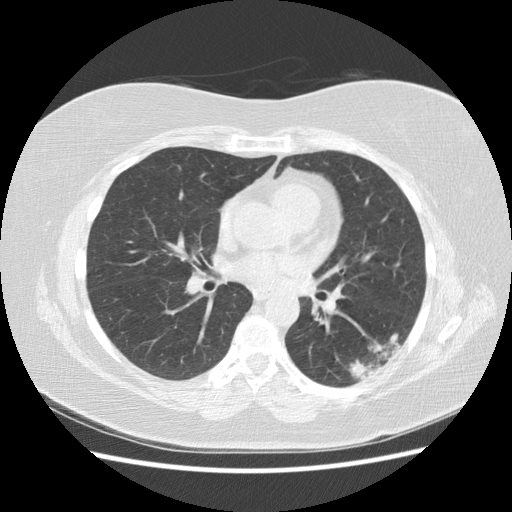
Low-dose screening chest CT, one axial slice. Slice 80 of 151 in the series (ordered by position). Reconstruction kernel STANDARD. 120 kVp. Lung window (W 1500 / L -600 HU). 2.5 mm slice thickness. 512 × 512 image matrix, field of view 360 × 360 mm.
Annotated regions visible in this slice (manually delineated by an expert):
- lesion 1 (tumor, lower lobe of left lung): bounding box <349,333,401,379> (left, top, right, bottom; pixels)